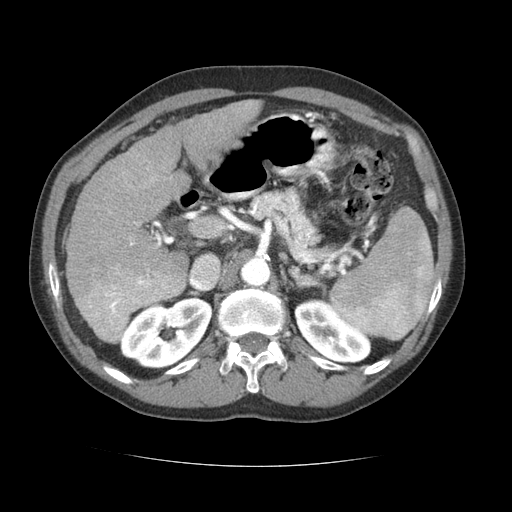
Contrast-enhanced abdominal CT (liver protocol), one axial slice. Slice 41 of 69 in the series (ordered by position). Reconstruction kernel STANDARD. Soft-tissue window (W 400 / L 40 HU). 2.5 mm slice thickness. 512 × 512 image matrix. From the clinical record (not read from this slice): diagnosis: hepatocellular carcinoma (patient treated with transarterial chemoembolisation; whether this scan precedes or follows treatment is not stated here); TNM stage (as recorded): Stage-II; Child-Pugh class: B; tumour differentiation: poorly differentiated; tumour nodularity: multinodular.
Outlined on this slice (semi-automatically segmented with operator editing):
- liver parenchyma outside the tumour (the mass and vessels are separate outlines, so this box may not span the whole liver): bounding box <66,100,261,326> (left, top, right, bottom; pixels)
- mass: <77,269,184,343>
- liver vessels: <116,169,160,269>